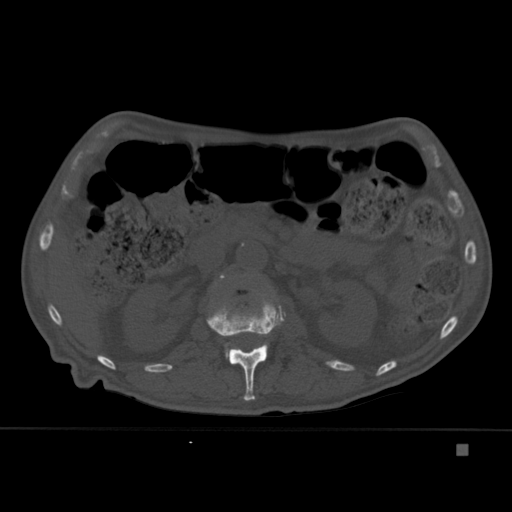
CT including the spine, one axial slice; slice 177 of 451 in the series (ordered by position); bone window (W 1800 / L 400 HU); 512 × 512 image matrix, field of view 378 × 378 mm. Patient: male, 75 years. Case-level facts recorded for this patient, not image findings: primary cancer: prostate.
Structures marked on this image (semi-automatic segmentation, software-assisted and operator-edited):
- L1 vertebra: bounding box (x1, y1, x2, y2) in pixels: (206, 293, 286, 401)
- L2 vertebra: (220, 275, 229, 358)